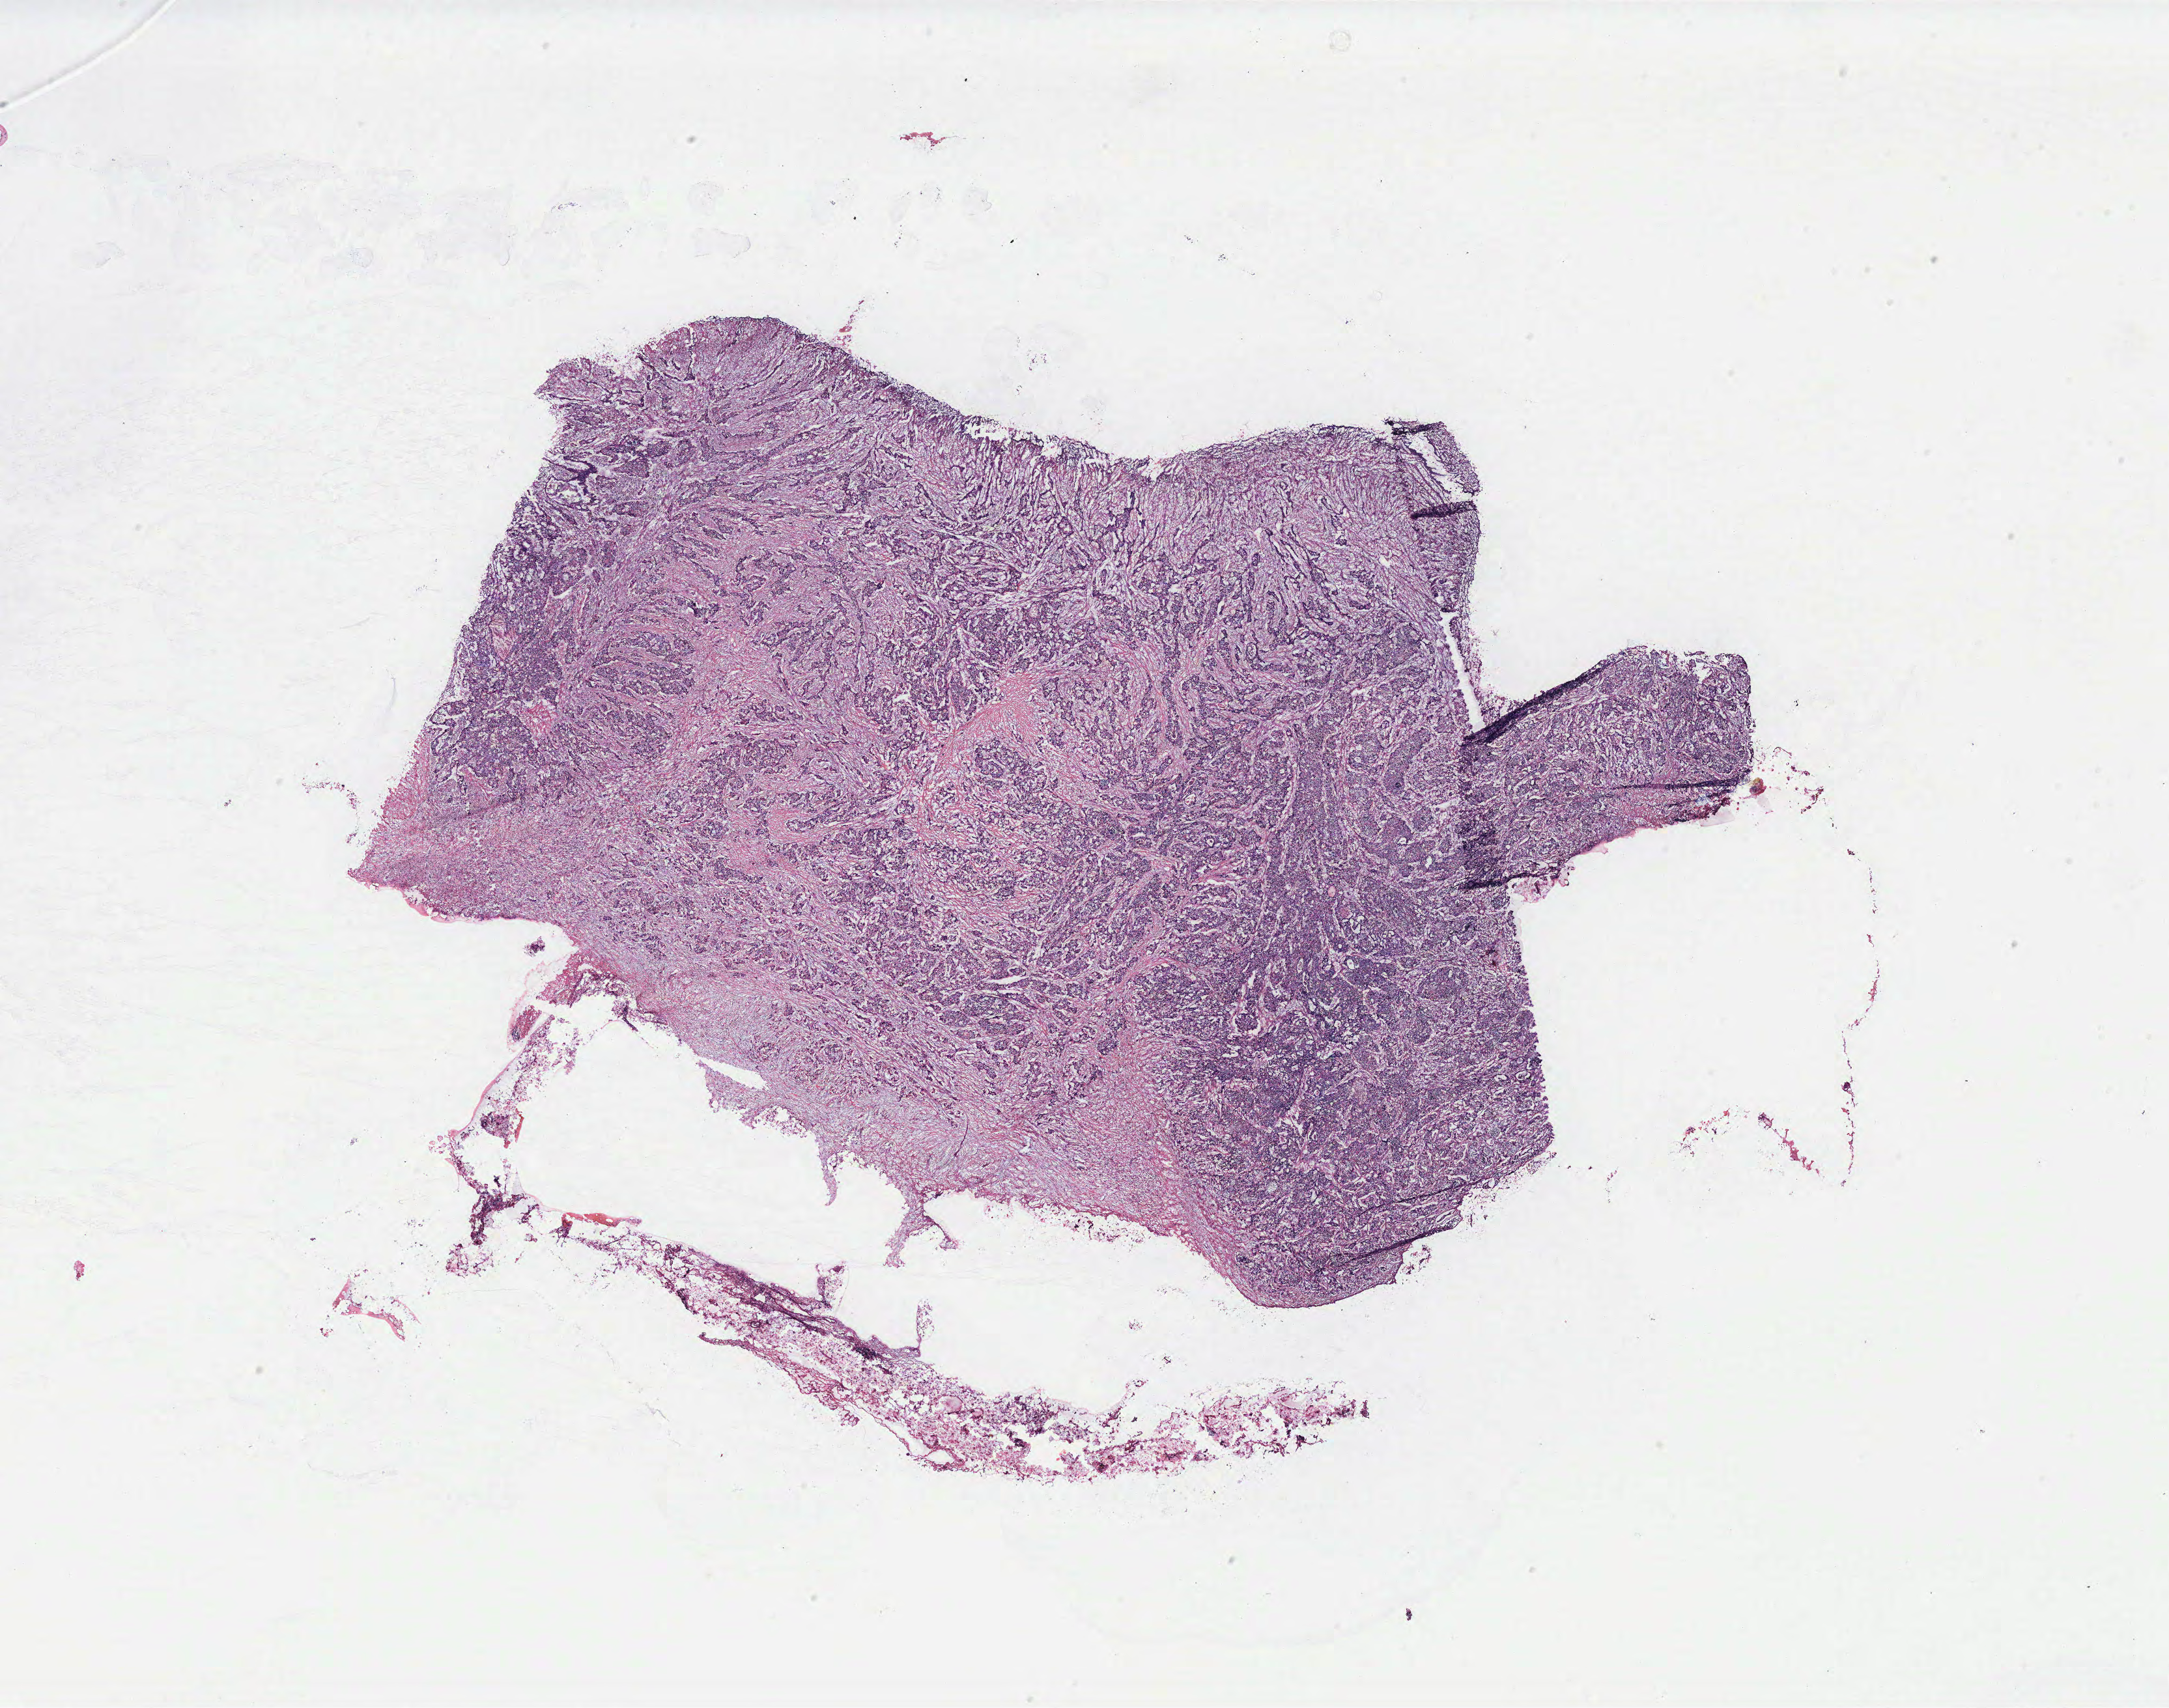
Whole-slide histology image, H&E-stained — a low-resolution overview of the entire scanned area, about 26.7 x 21.0 mm (from a 40x scan), colon, normal (non-tumour) tissue. Patient: female, age 67 years.
This section: normal (non-tumour) tissue from the same patient. Patient diagnosis: Adenocarcinoma, NOS.